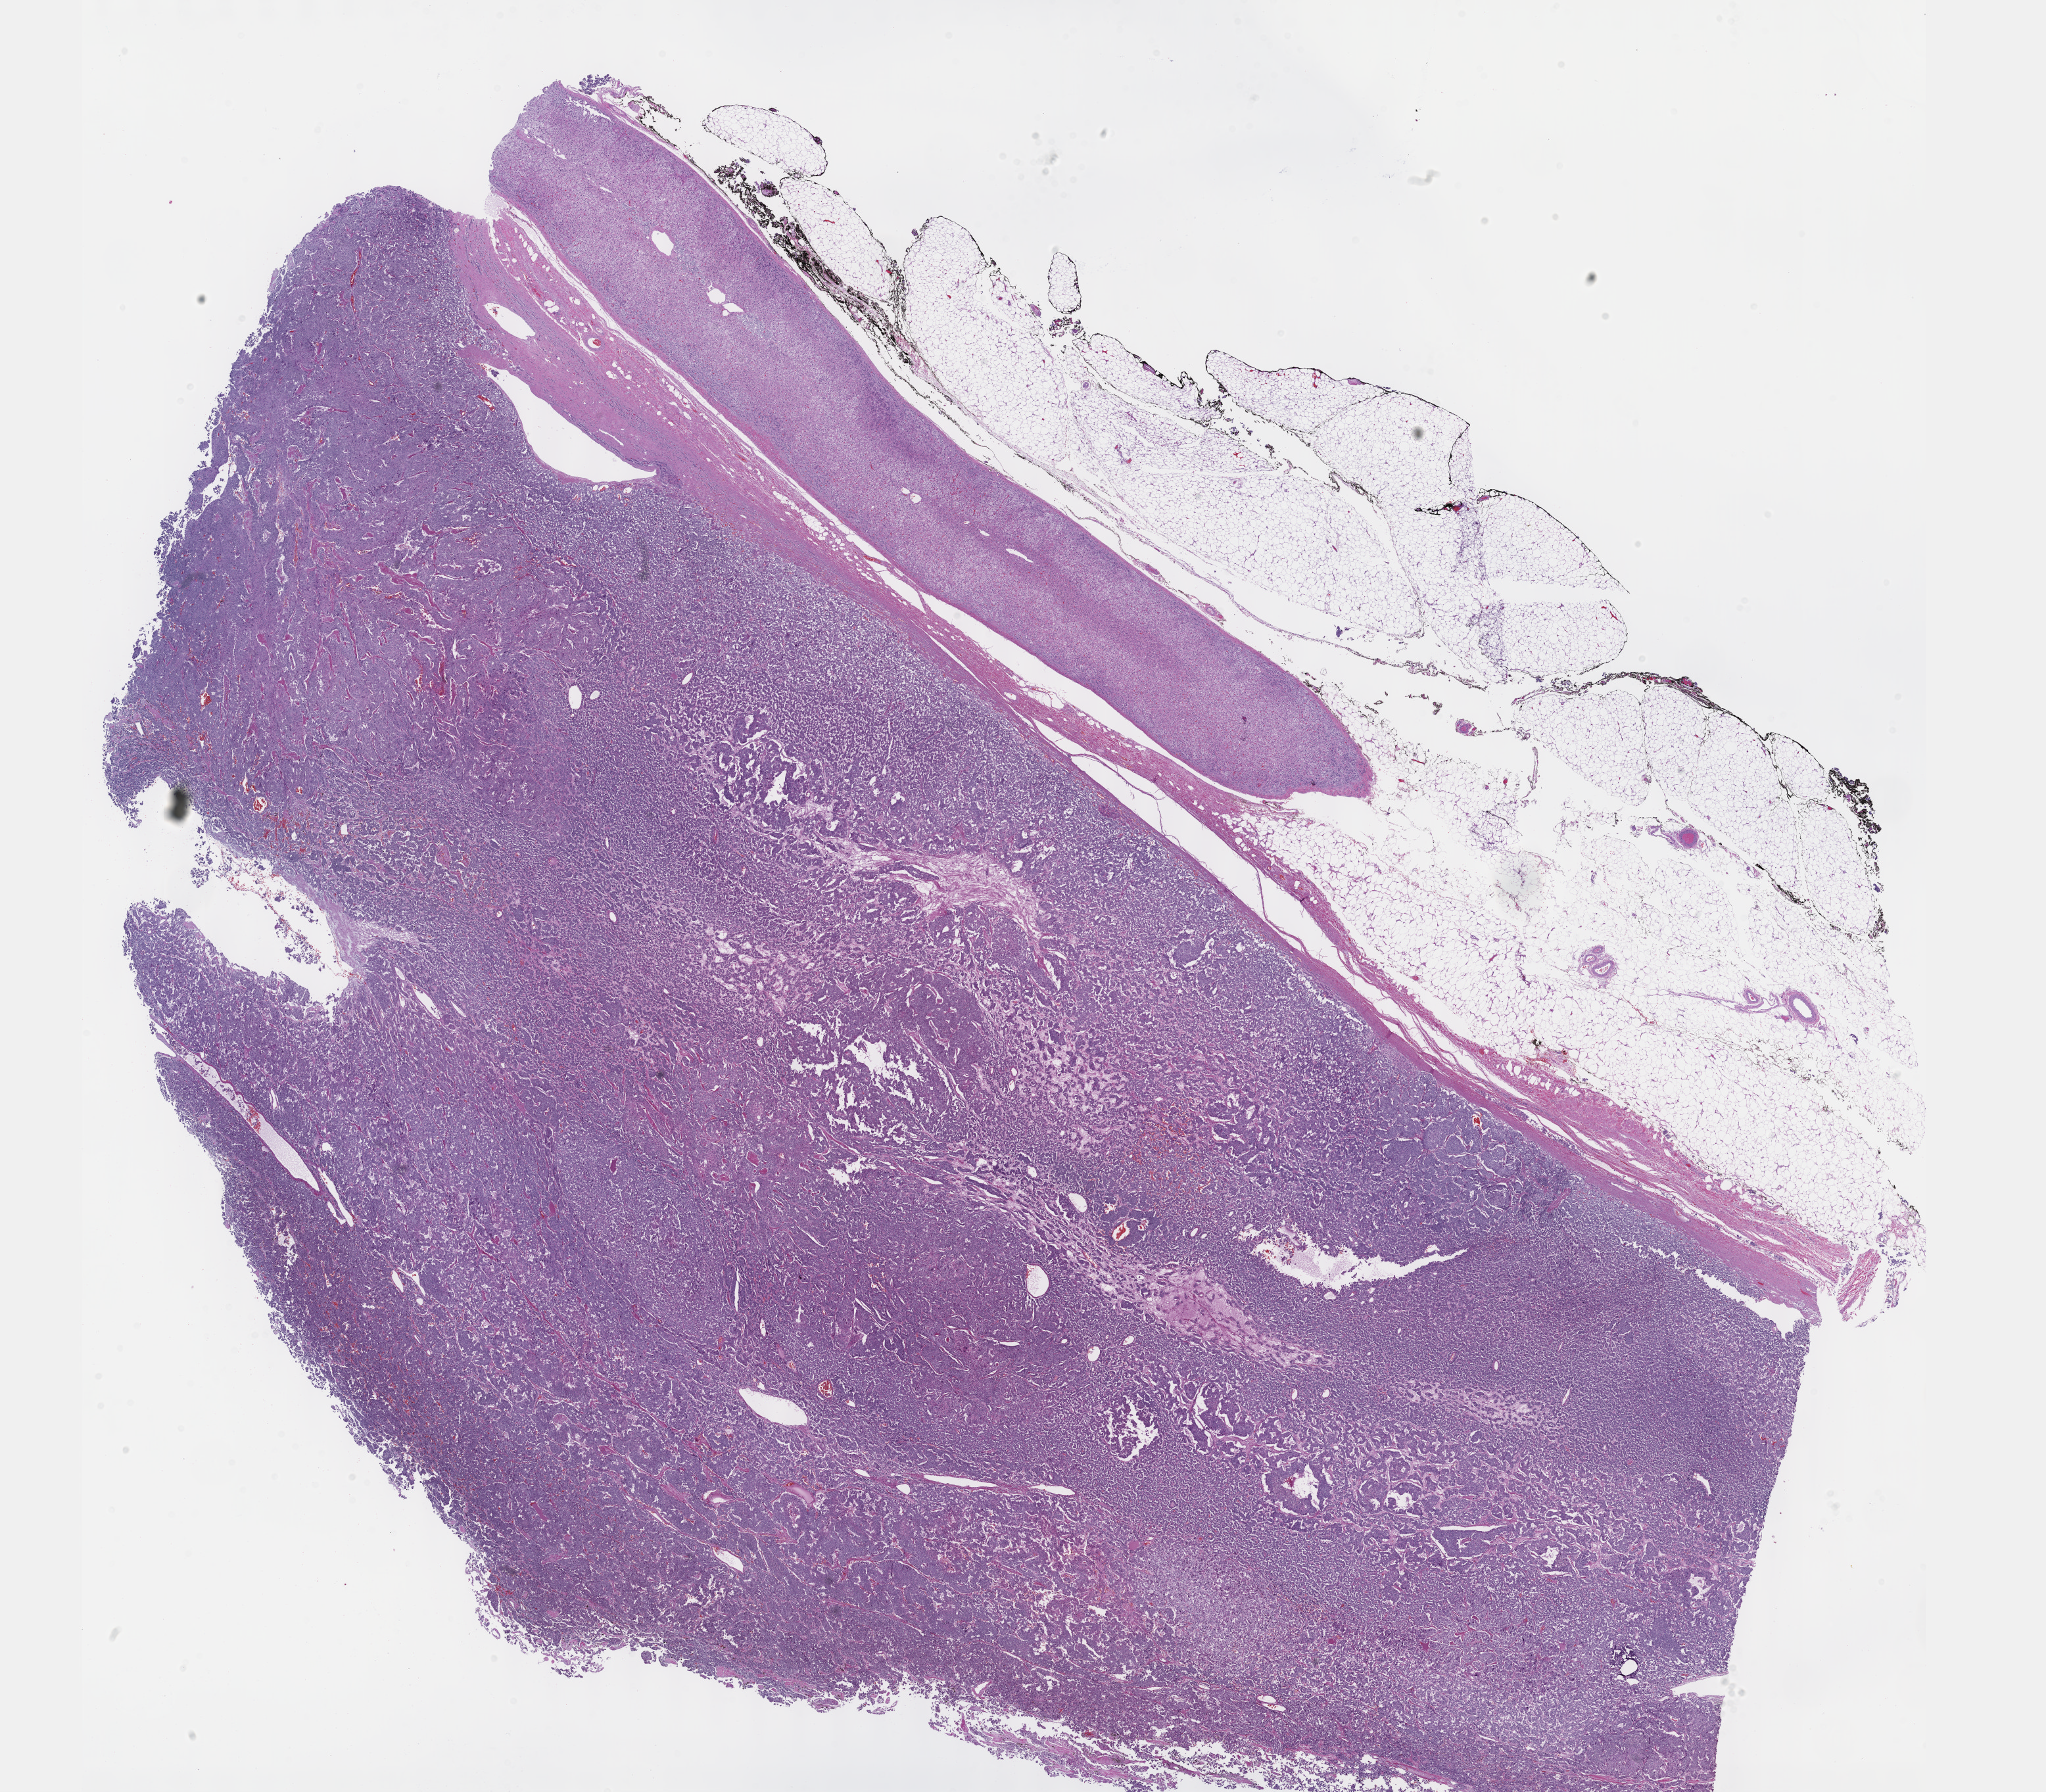
Hematoxylin and eosin (H&E) stained whole-slide image — low-resolution overview of the scanned area, about 25.1 x 22.0 mm (acquisition: 40x scan). Formalin-fixed paraffin-embedded (FFPE) diagnostic section. Adrenal gland, primary tumour sample. Patient: female, age at initial diagnosis 43 years.
• pathologic diagnosis: Pheochromocytoma, NOS